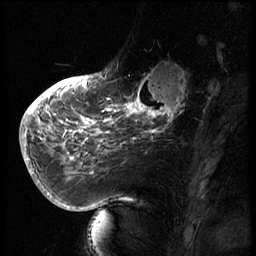
Breast MRI (dynamic contrast-enhanced), one sagittal slice. Position 21 of 66 along the scan axis. 3 images stored at this slice position (order not interpretable as contrast timing). 1.5 T. TE 4.2 ms, TR 8.9 ms. 2.5 mm slice thickness. 256 × 256 image matrix, field of view 200 × 200 mm. Patient: female, 56 years. Case-level facts recorded for this patient, not image findings: setting: breast cancer imaged before/during neoadjuvant chemotherapy.
Annotated regions visible in this slice (semi-automatic segmentation, software-assisted and operator-edited):
- analysis volume of interest (the breast-tissue region the enhancement analysis was run in; not a lesion): bounding box (x1, y1, x2, y2) in pixels: (129, 63, 194, 127)
- tumour enhancement mask (voxels above the 140 % enhancement threshold inside the analysis volume of interest): (129, 66, 188, 127)